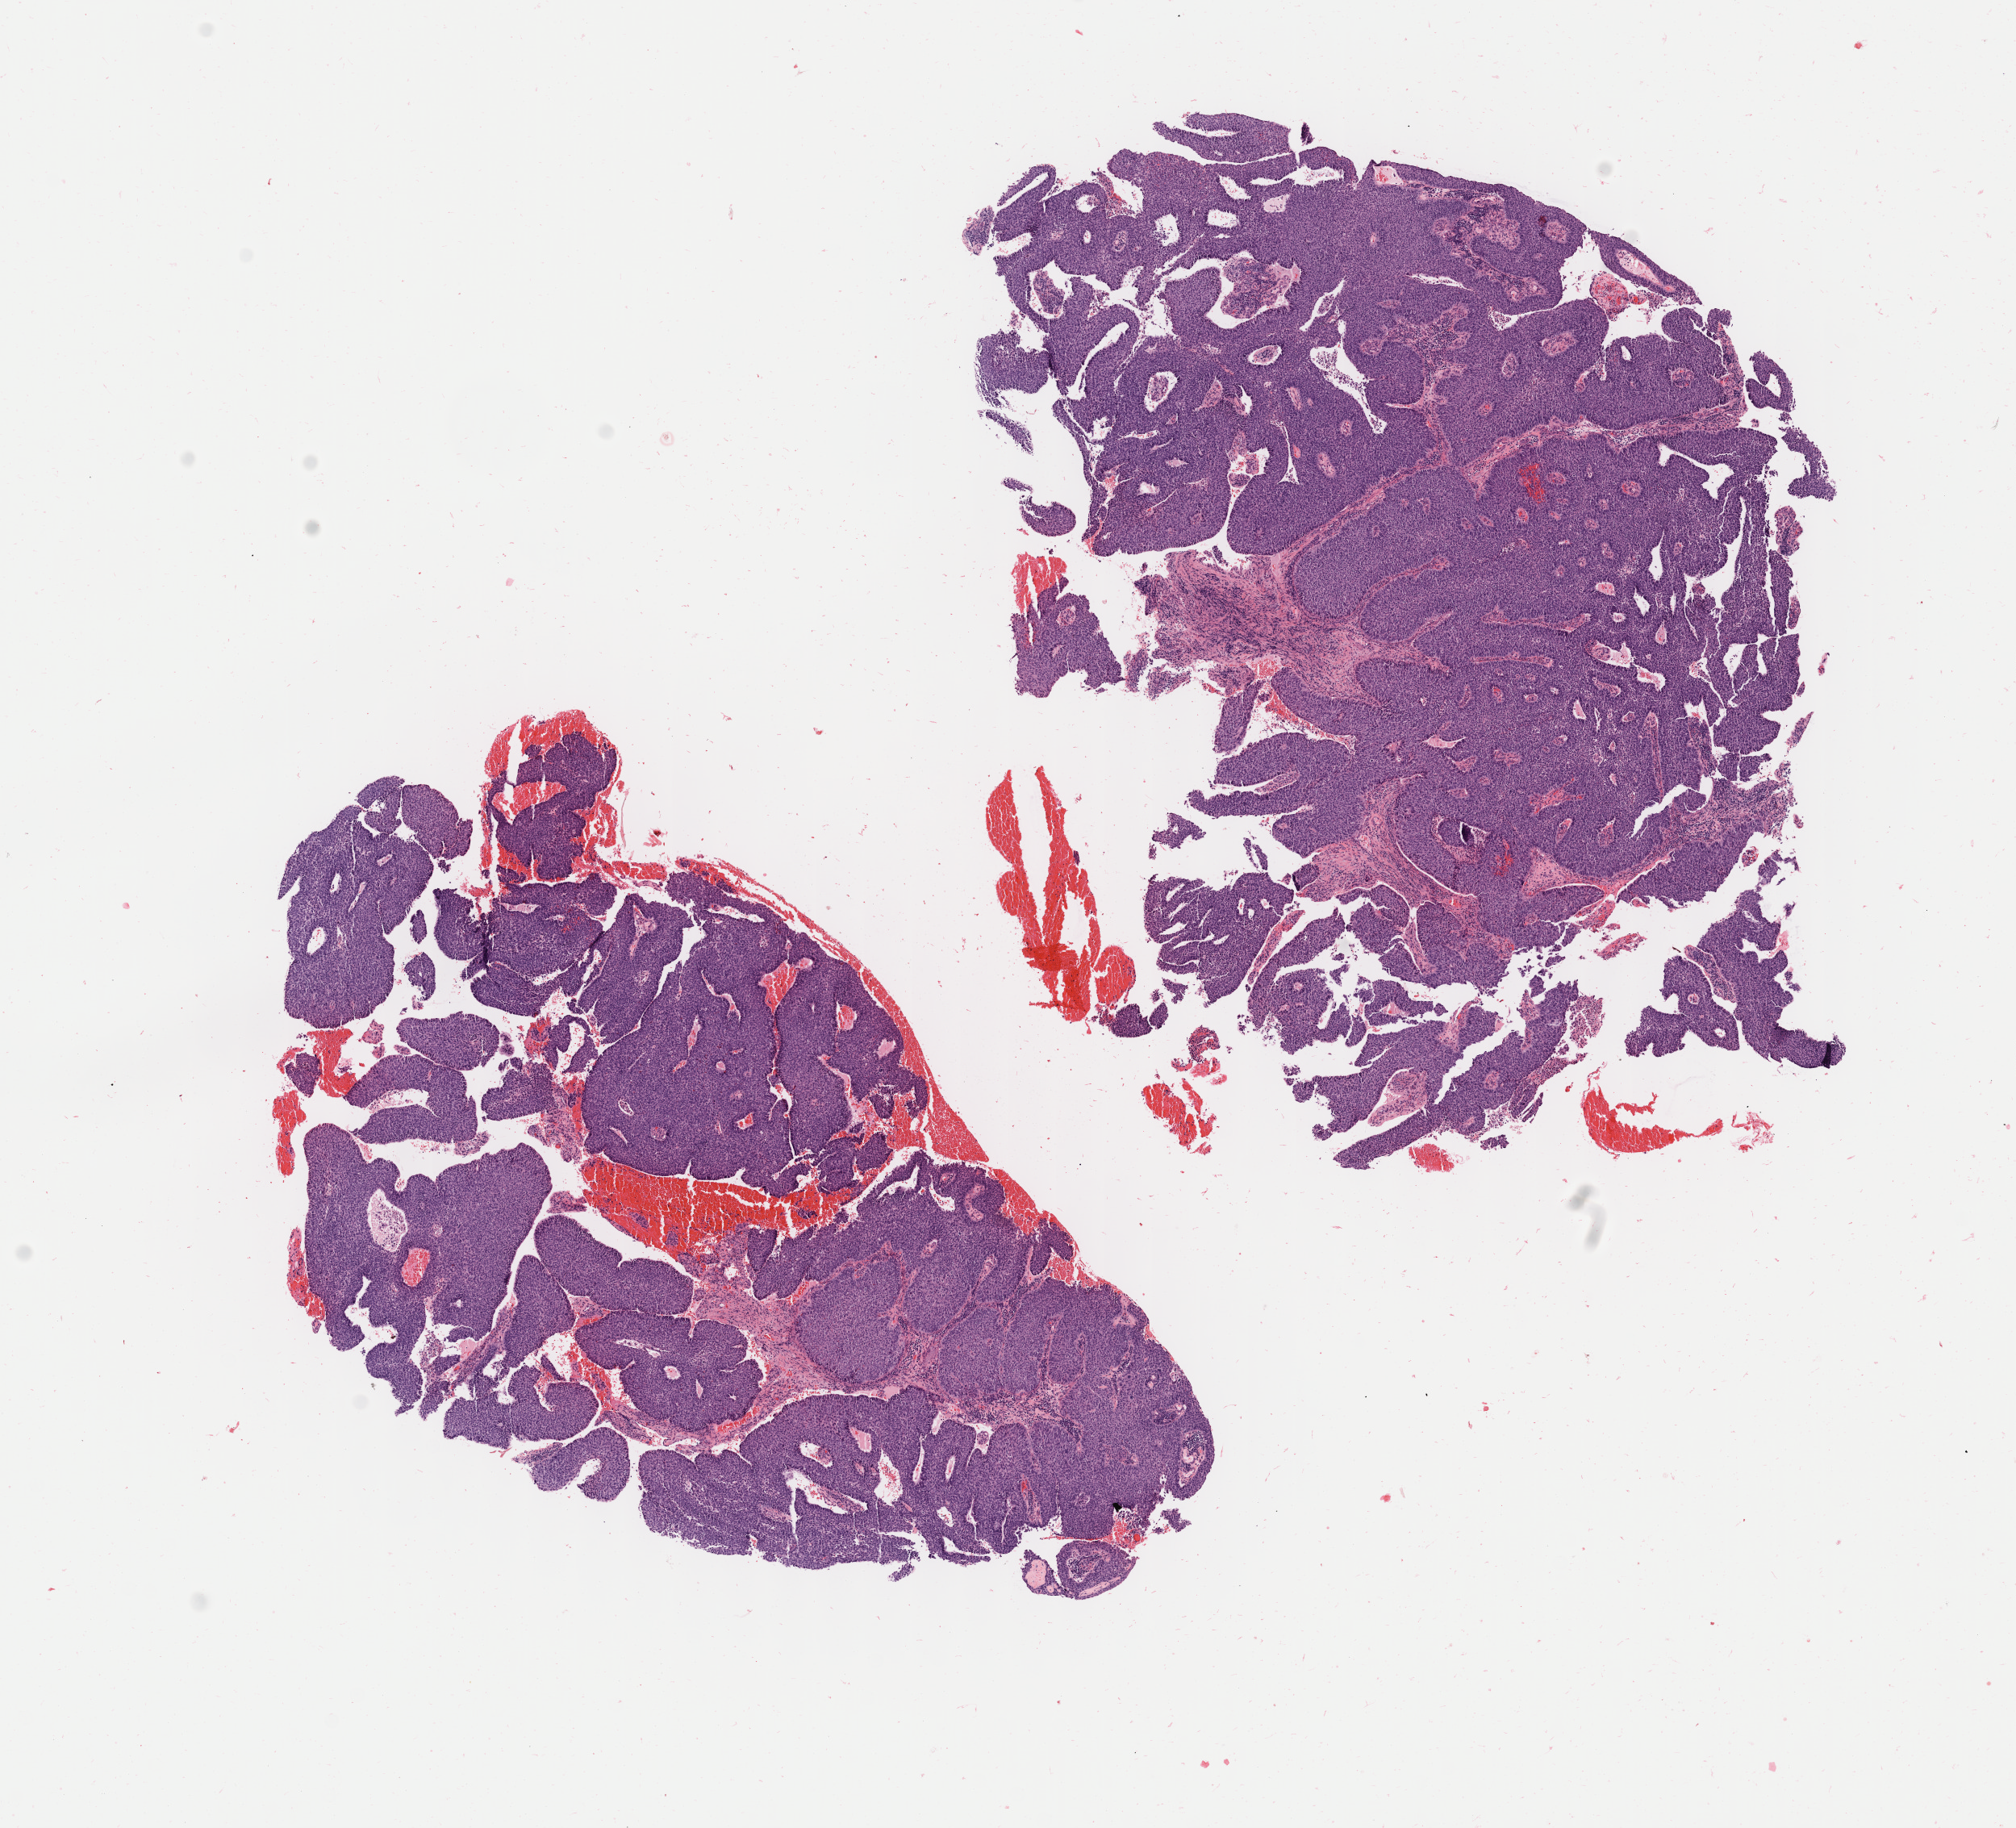
Whole-slide image, hematoxylin and eosin (H&E) stain — whole scanned area (about 9.9 x 9.0 mm) shown as a low-resolution overview, tumor tissue, site: cervix. Patient: female, aged 78.
Diagnosis: Squamous cell carcinoma, large cell, nonkeratinizing, NOS.